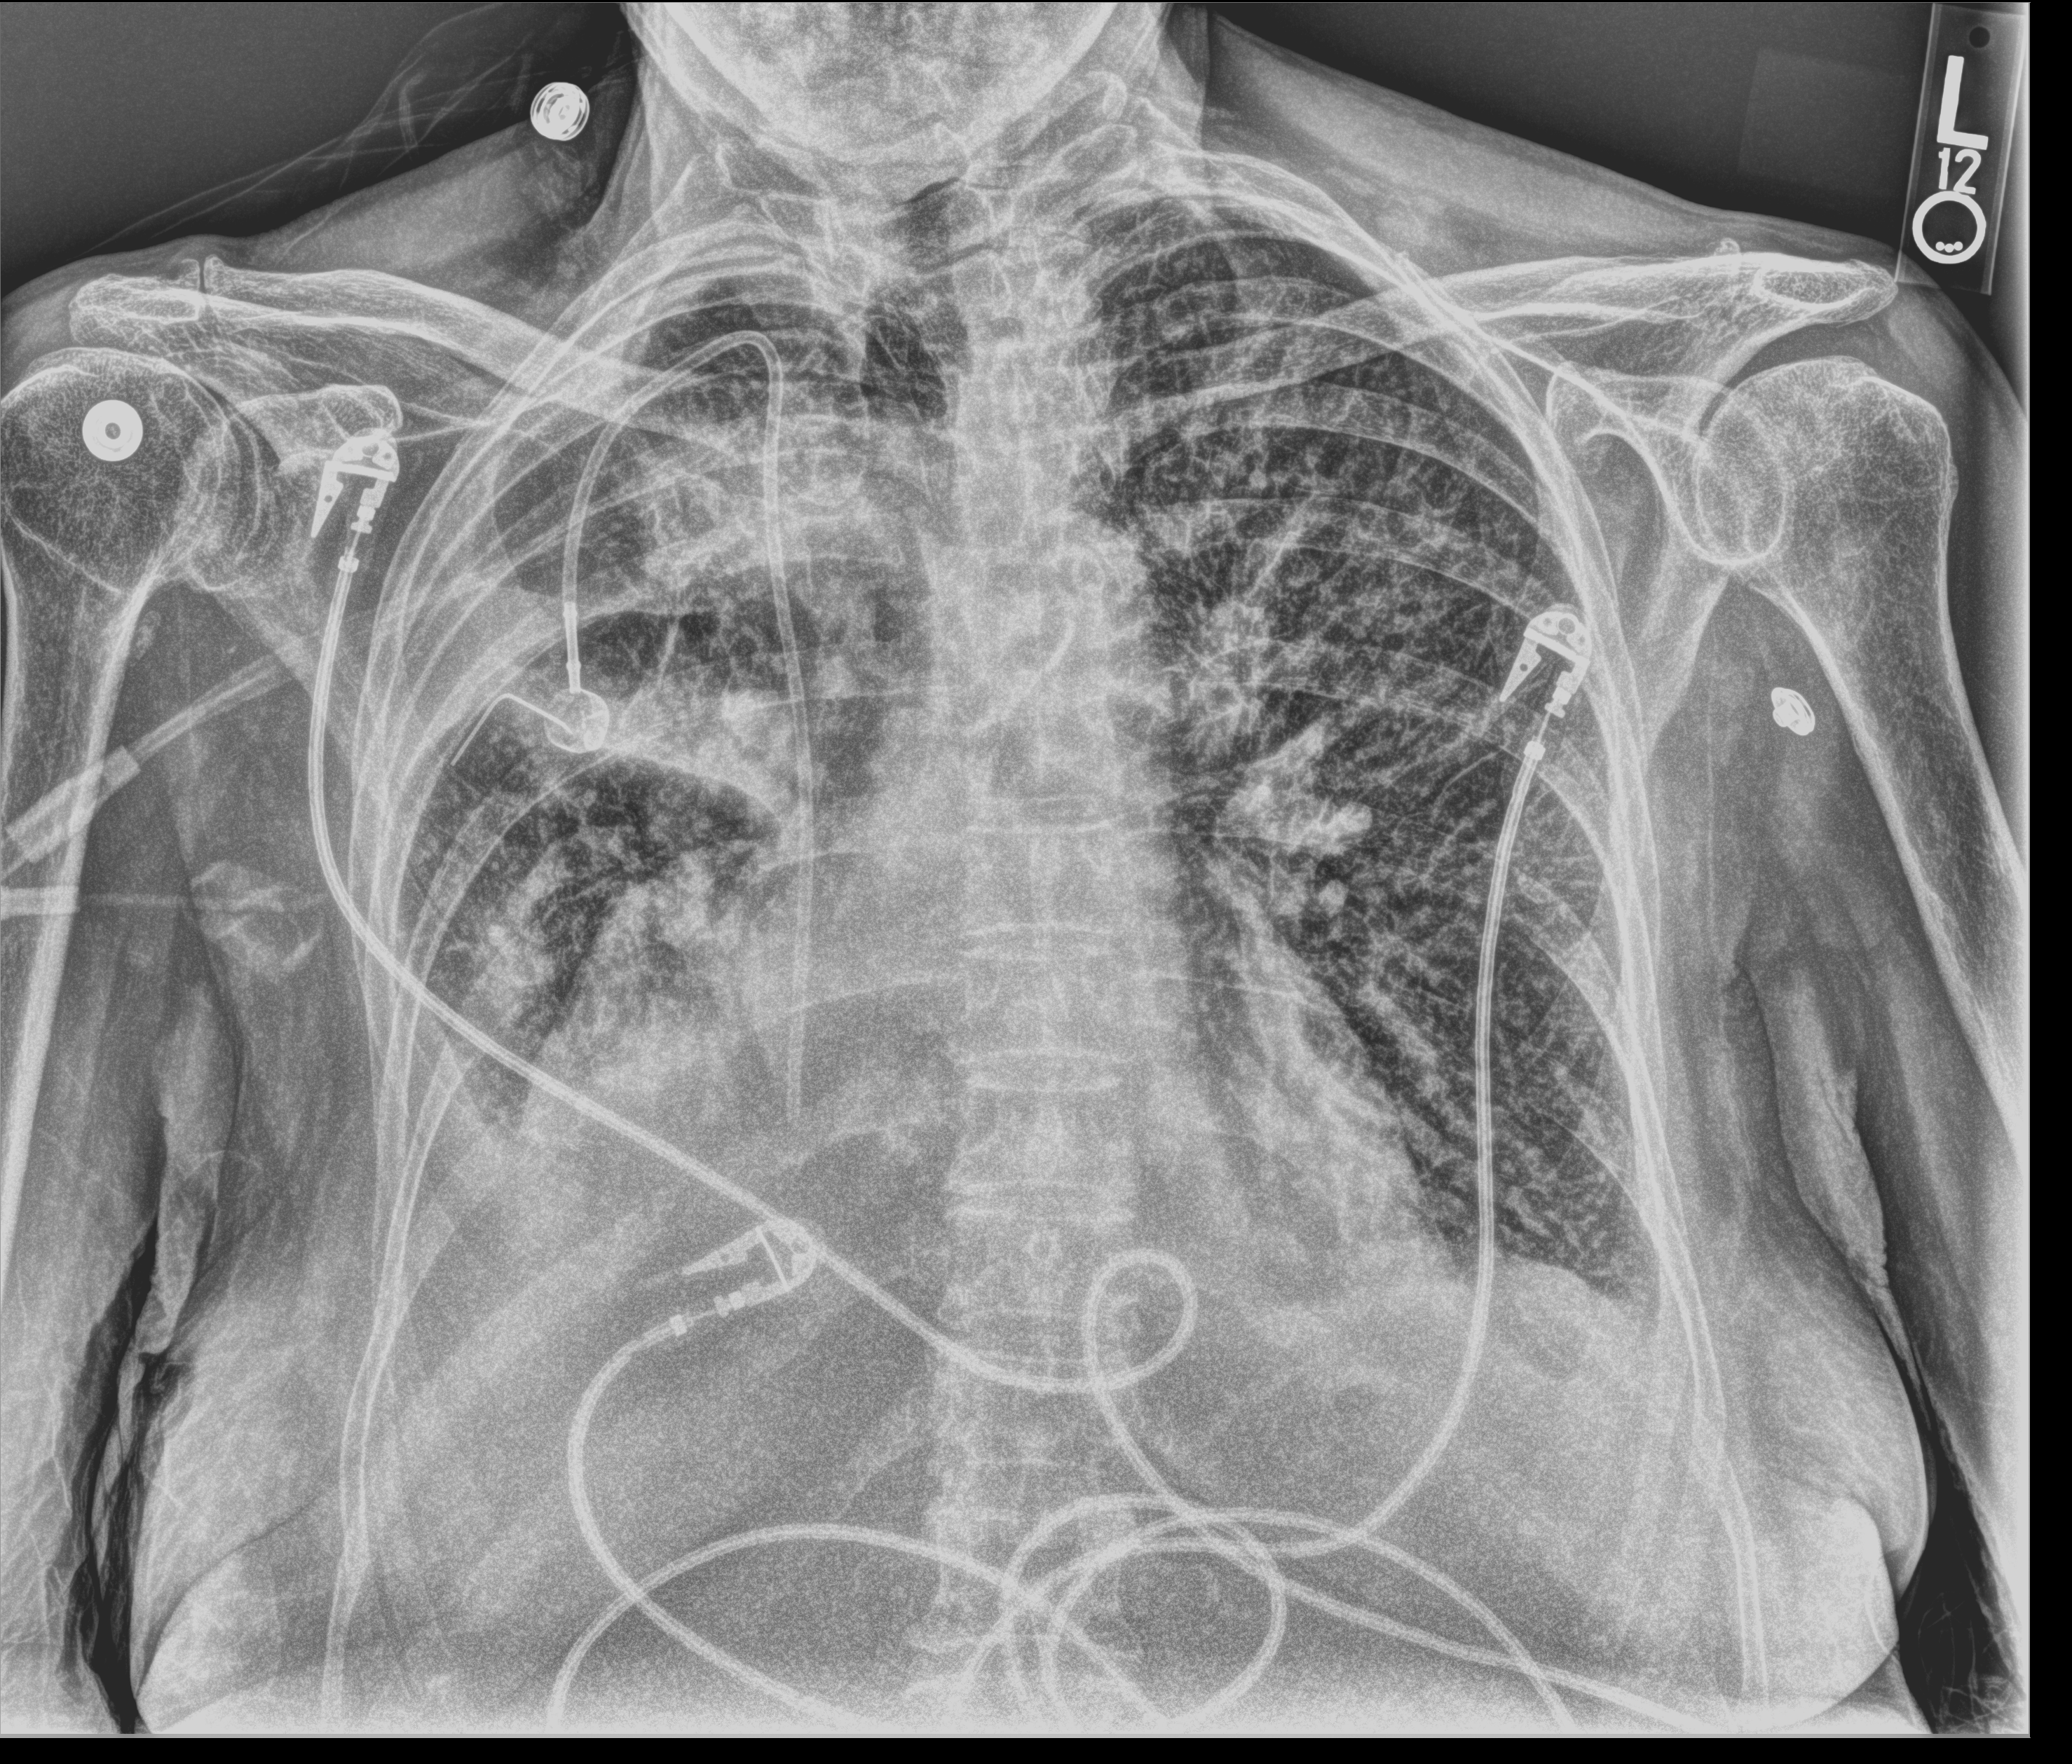
Portable chest radiograph, anteroposterior (AP) projection. Patient hospitalised with COVID-19; female, aged 60–74 years.
Admission-level facts for this patient (not findings on this image; timing relative to this image not recorded): admitted to intensive care during this hospital stay: no; mechanically ventilated during this hospital stay: no.